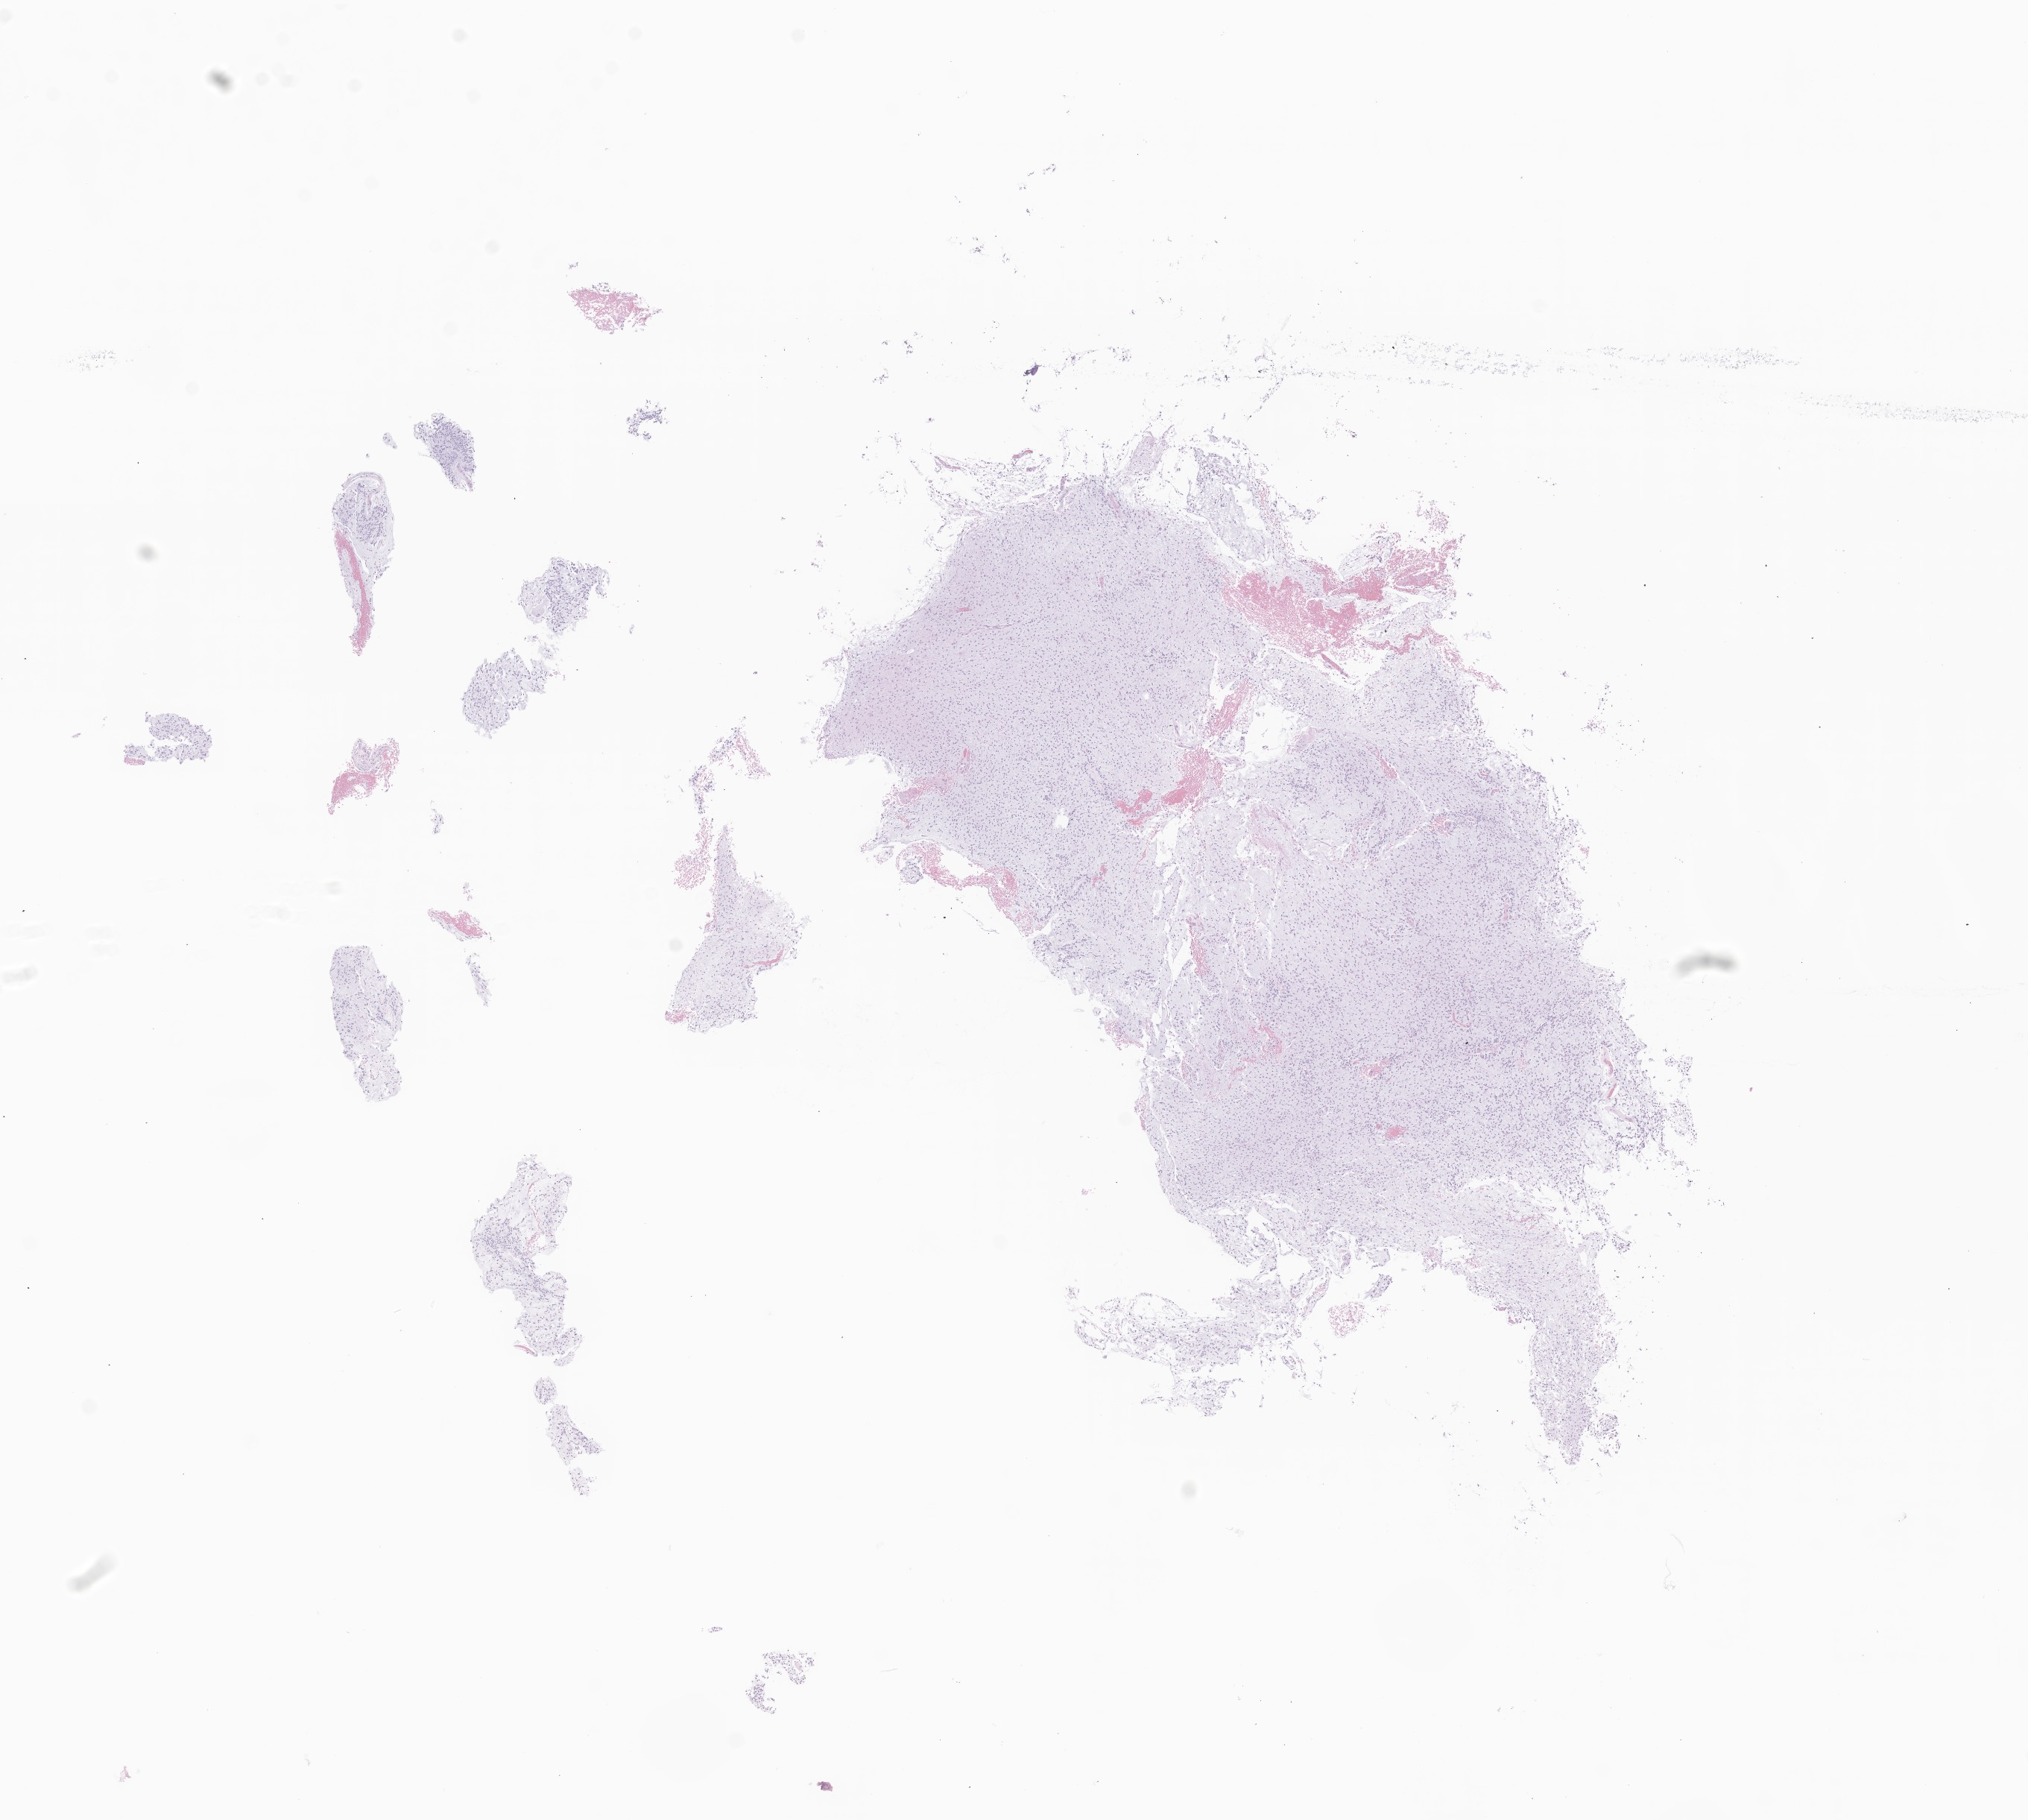
Whole-slide image, hematoxylin and eosin (H&E) stain of tumor tissue from the spinal cord, low-resolution overview of the scanned area, about 11.5 x 10.3 mm. Patient male; age 49 months (4 years 1 month).
- specimen: formalin-fixed, paraffin-embedded (FFPE) tissue